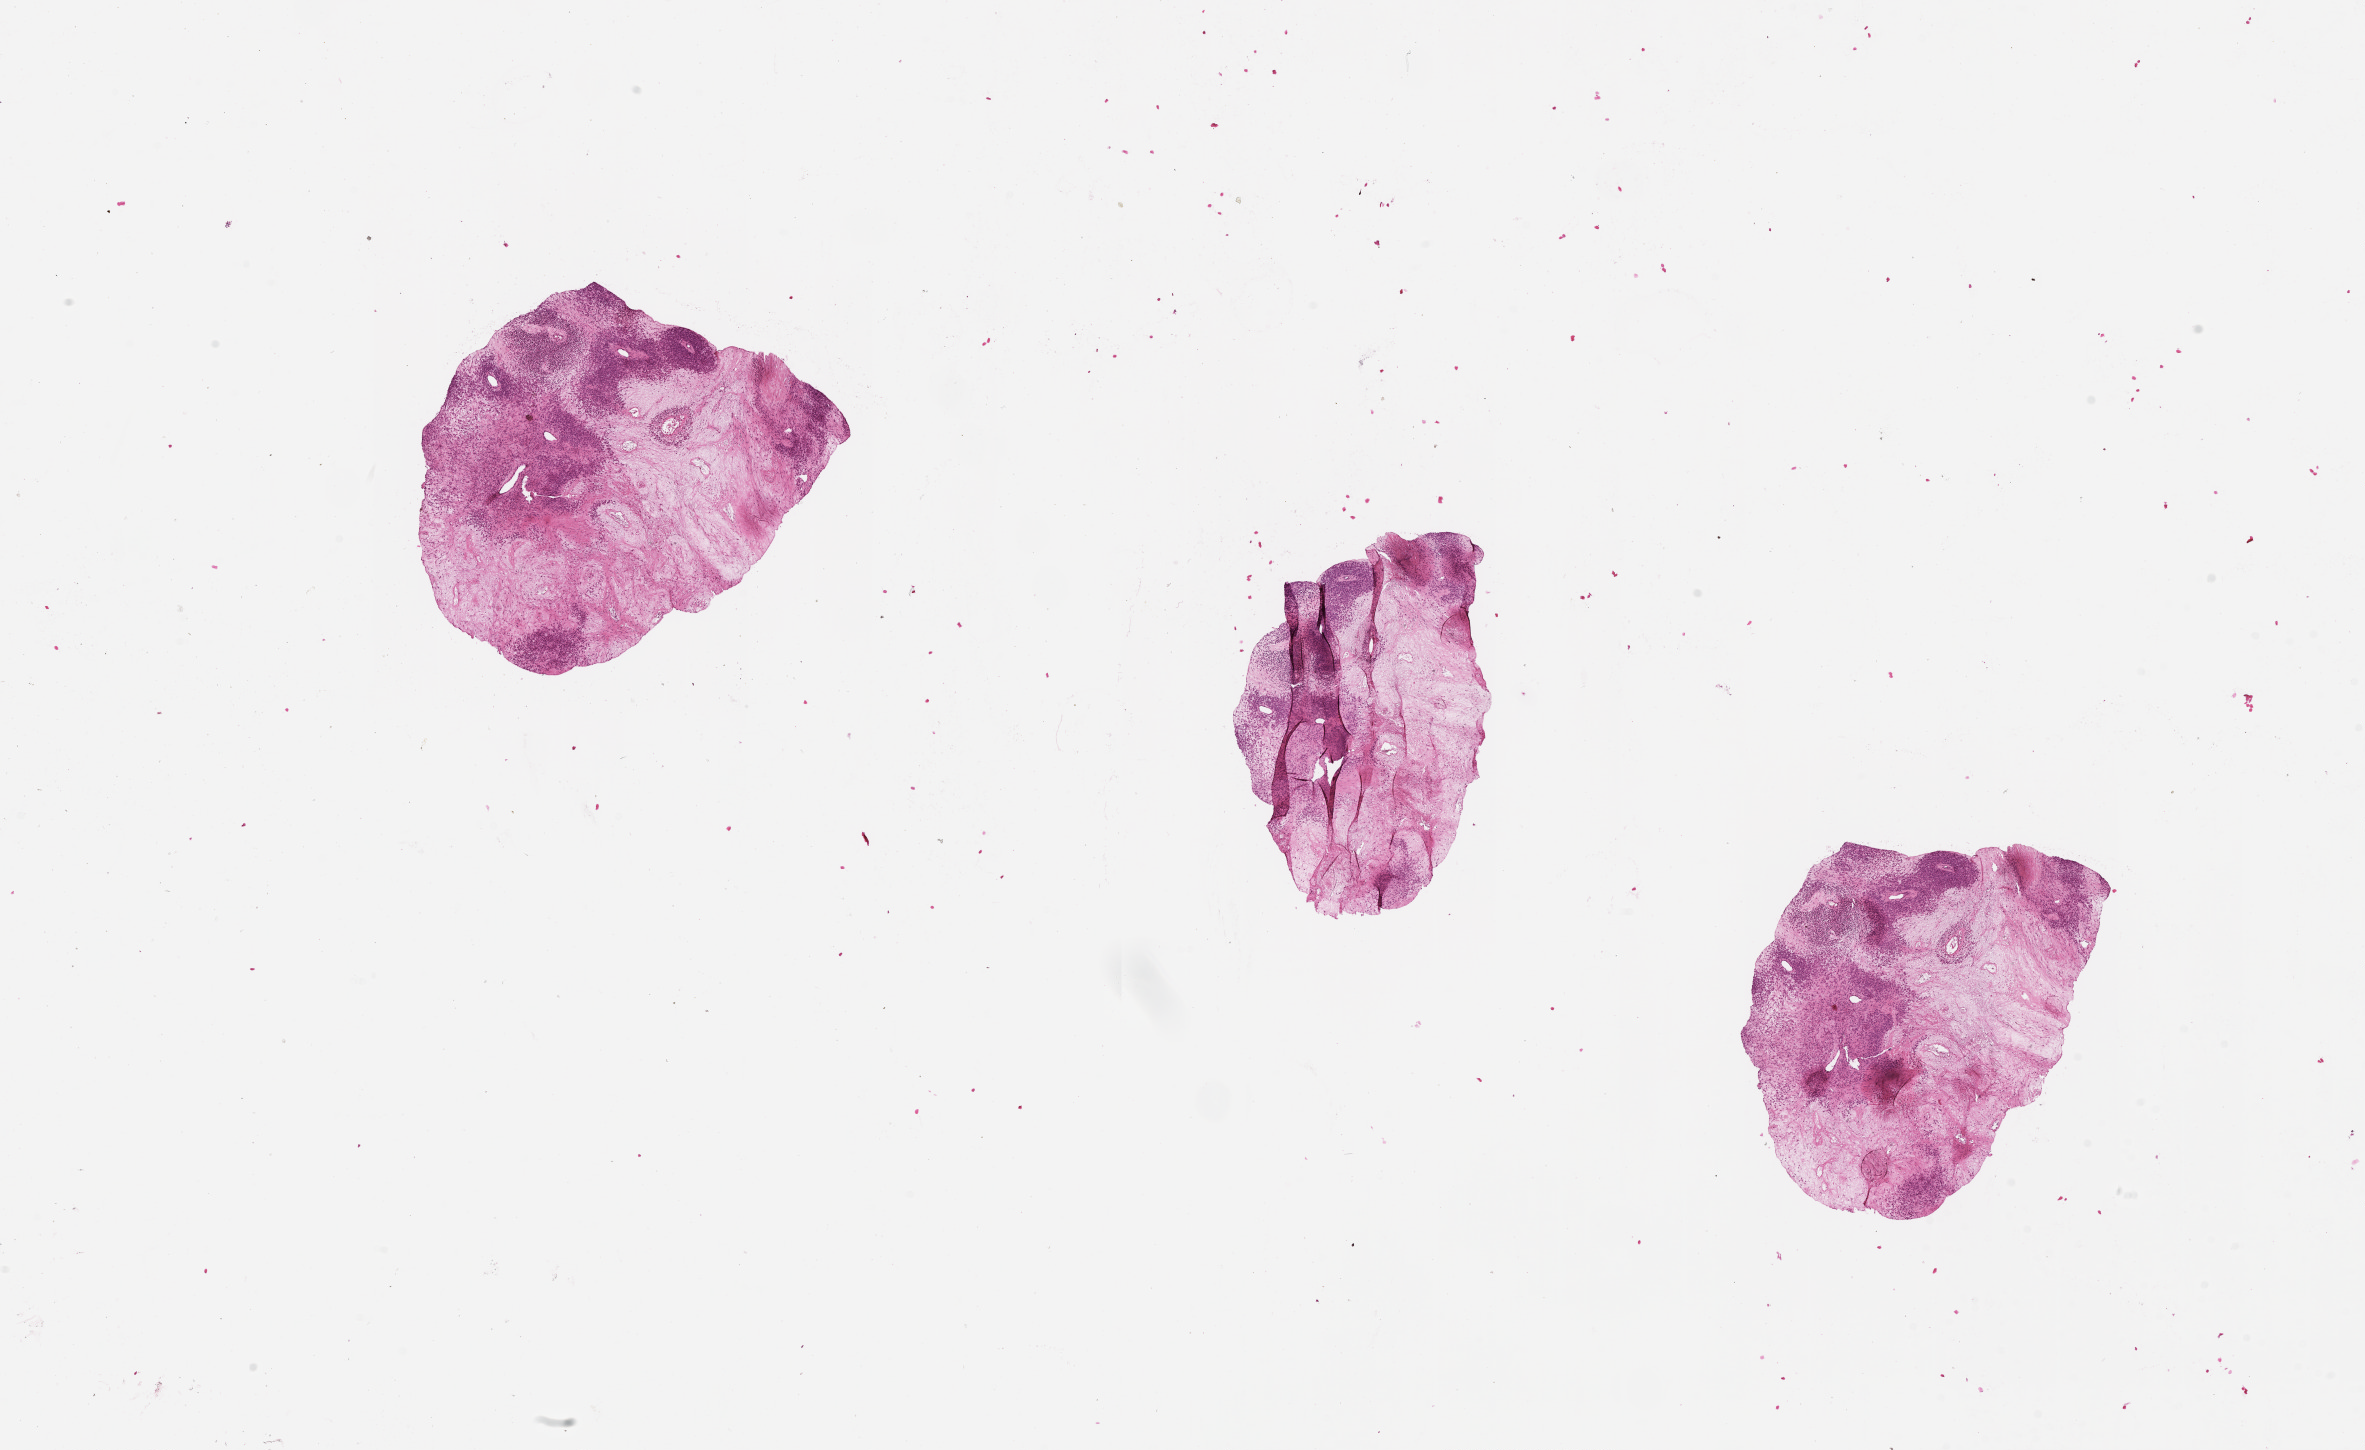
Hematoxylin and eosin (H&E) stained whole-slide image, shown as a low-resolution overview of the whole scanned area (about 19.0 x 11.7 mm); tumour tissue sample, sampled site: lymph node. Male, 57 y/o. Slide review estimates, as recorded: tumour nuclei 80%, necrosis 0%.
• this section: metastatic tumour tissue
• patient diagnosis: Malignant melanoma, NOS